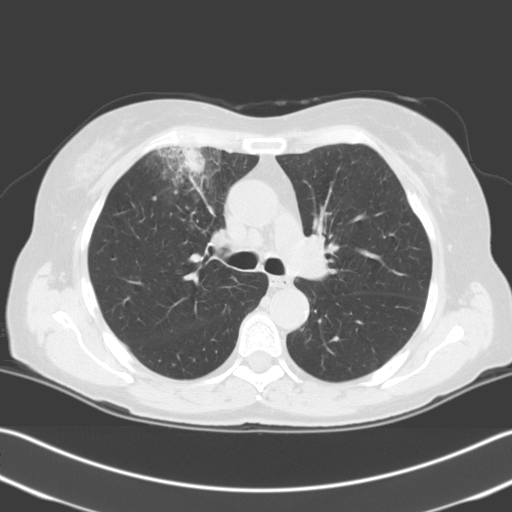
Low-dose screening chest CT, one axial slice. Position 140 of 204 along the scan axis. 140 kVp. Lung window (W 1500 / L -600 HU). 3.2 mm slice thickness. 512 × 512 image matrix, field of view 348 × 348 mm.
Outlined on this slice (manually delineated by an expert):
- lesion 1 (tumor, upper lobe of right lung): box from (x=175, y=148) to (x=205, y=174) px